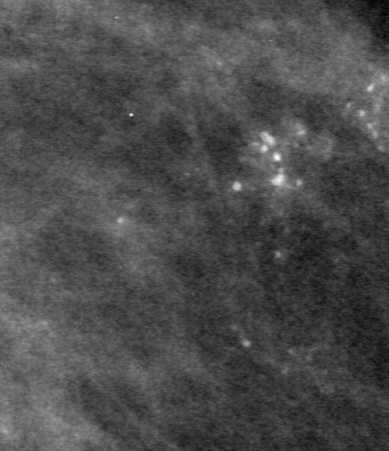
Cropped region of a digitized screen-film mammogram centred on a radiologist-marked abnormality, right breast, MLO view.
Marked abnormality: calcifications, morphology pleomorphic, distribution segmental; BI-RADS assessment category 4; subtlety rating 4 on a 1 (subtle) to 5 (obvious) scale; pathology result (as recorded, not read from the image): malignant.